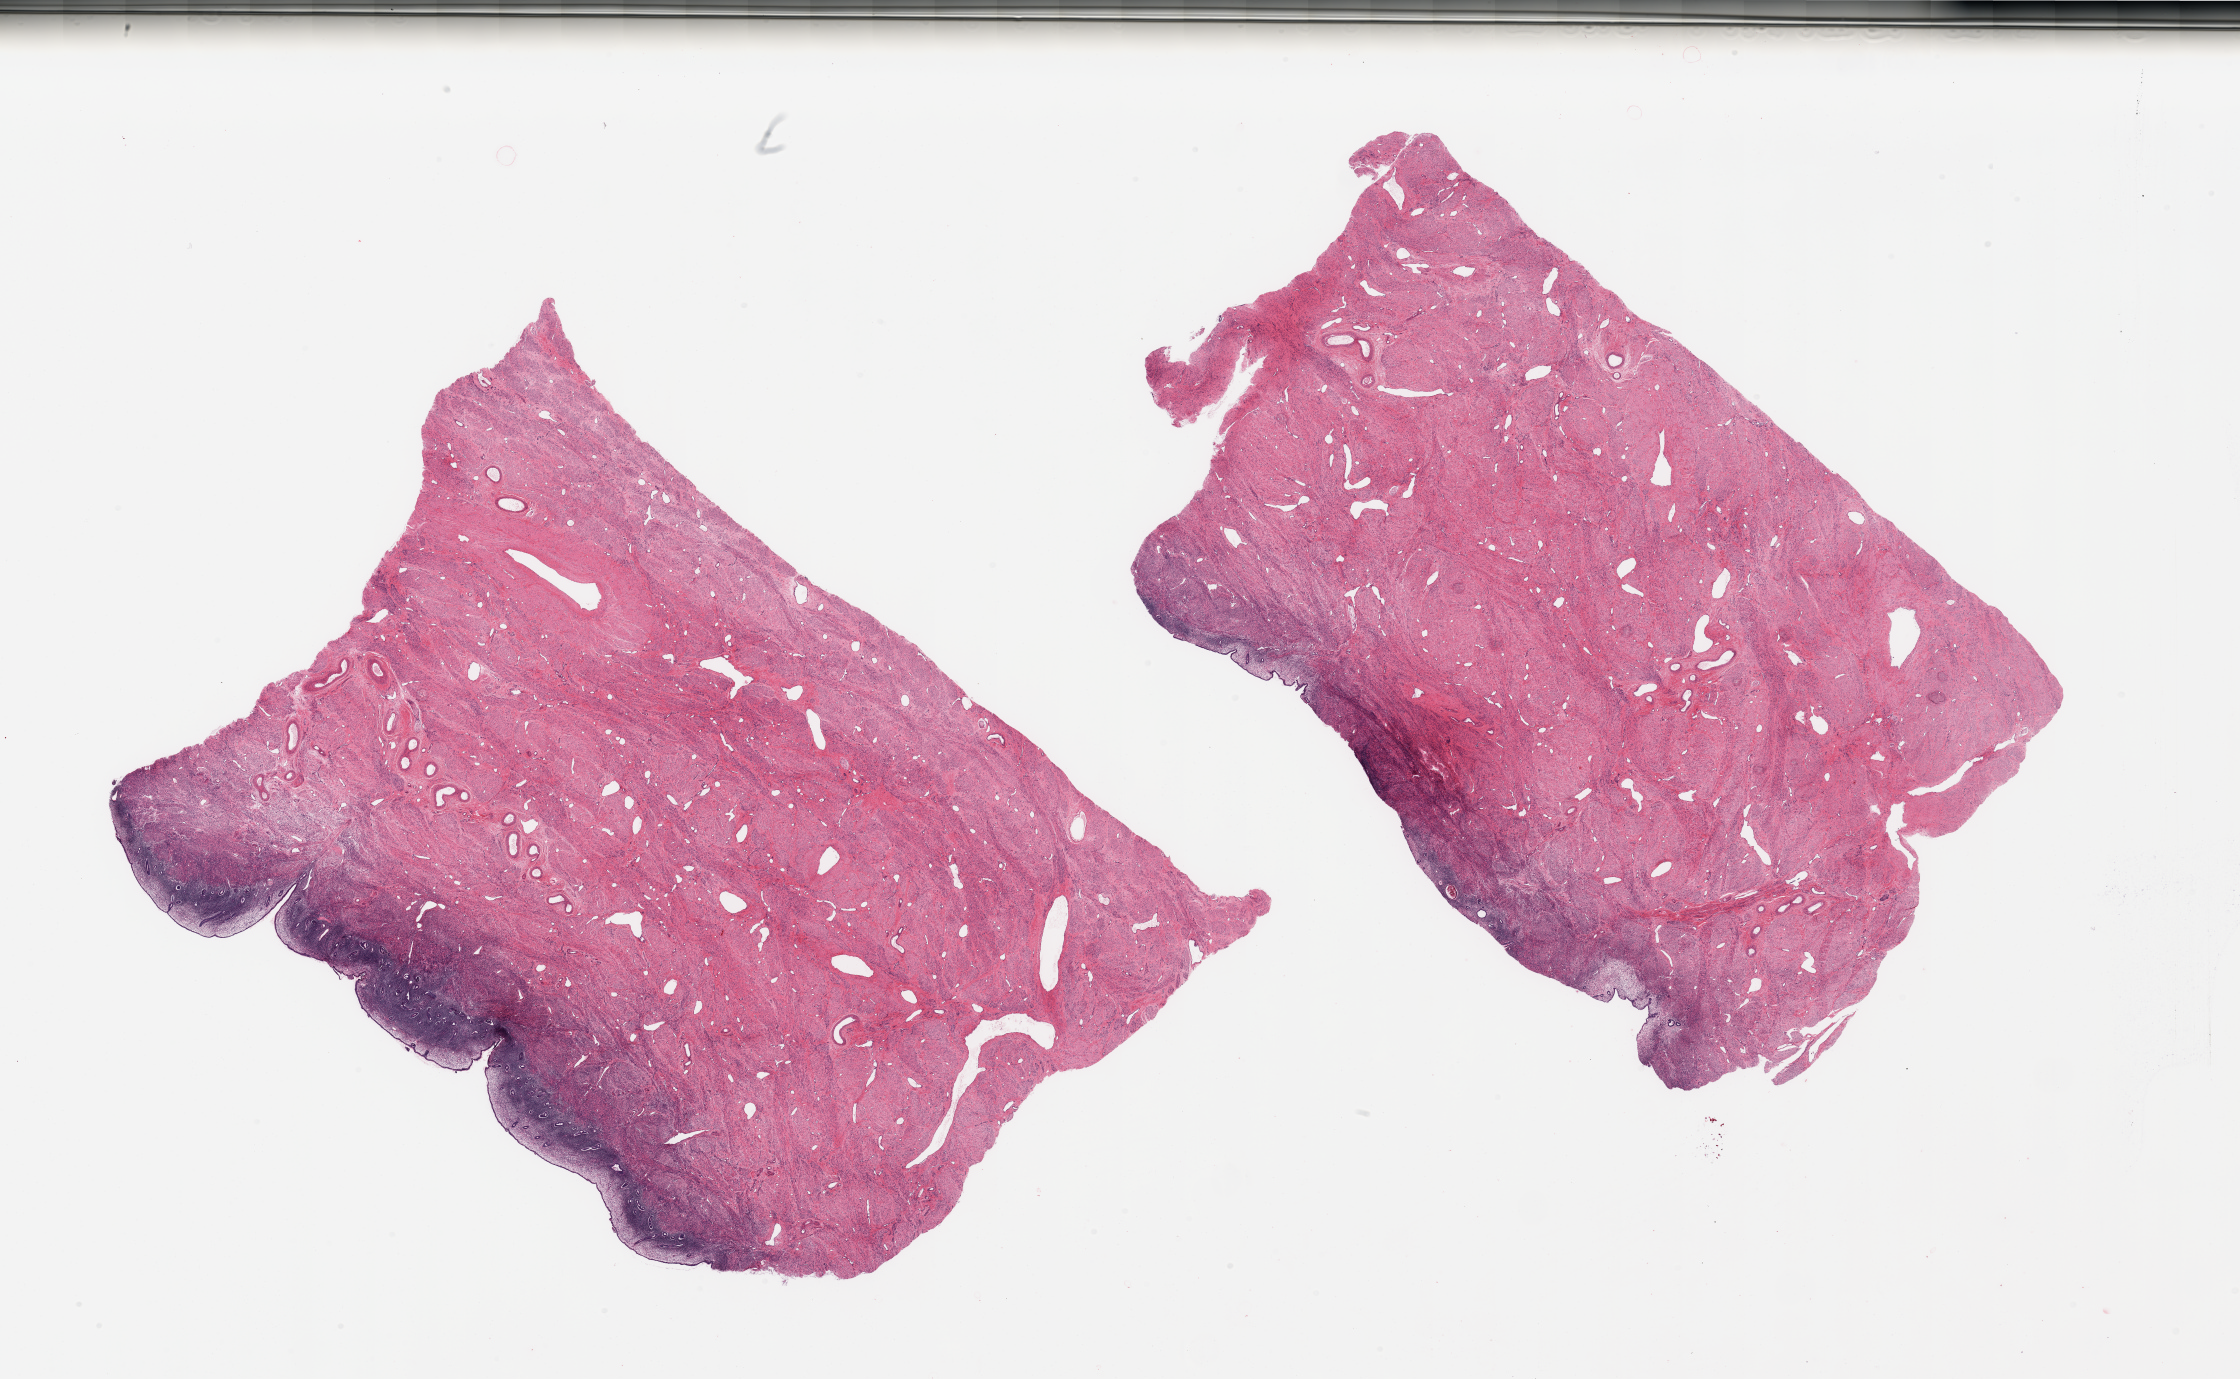
H&E whole-slide image — whole scanned area (about 35.4 x 21.8 mm) shown as a low-resolution overview. PAXgene-fixed, paraffin-embedded tissue. Sampled site (target tissue): uterus. Donor tissue sample.
Reviewer comment on this tissue sample: 2 pieces; endometrium (up to ~1mm thick) and myometrium.